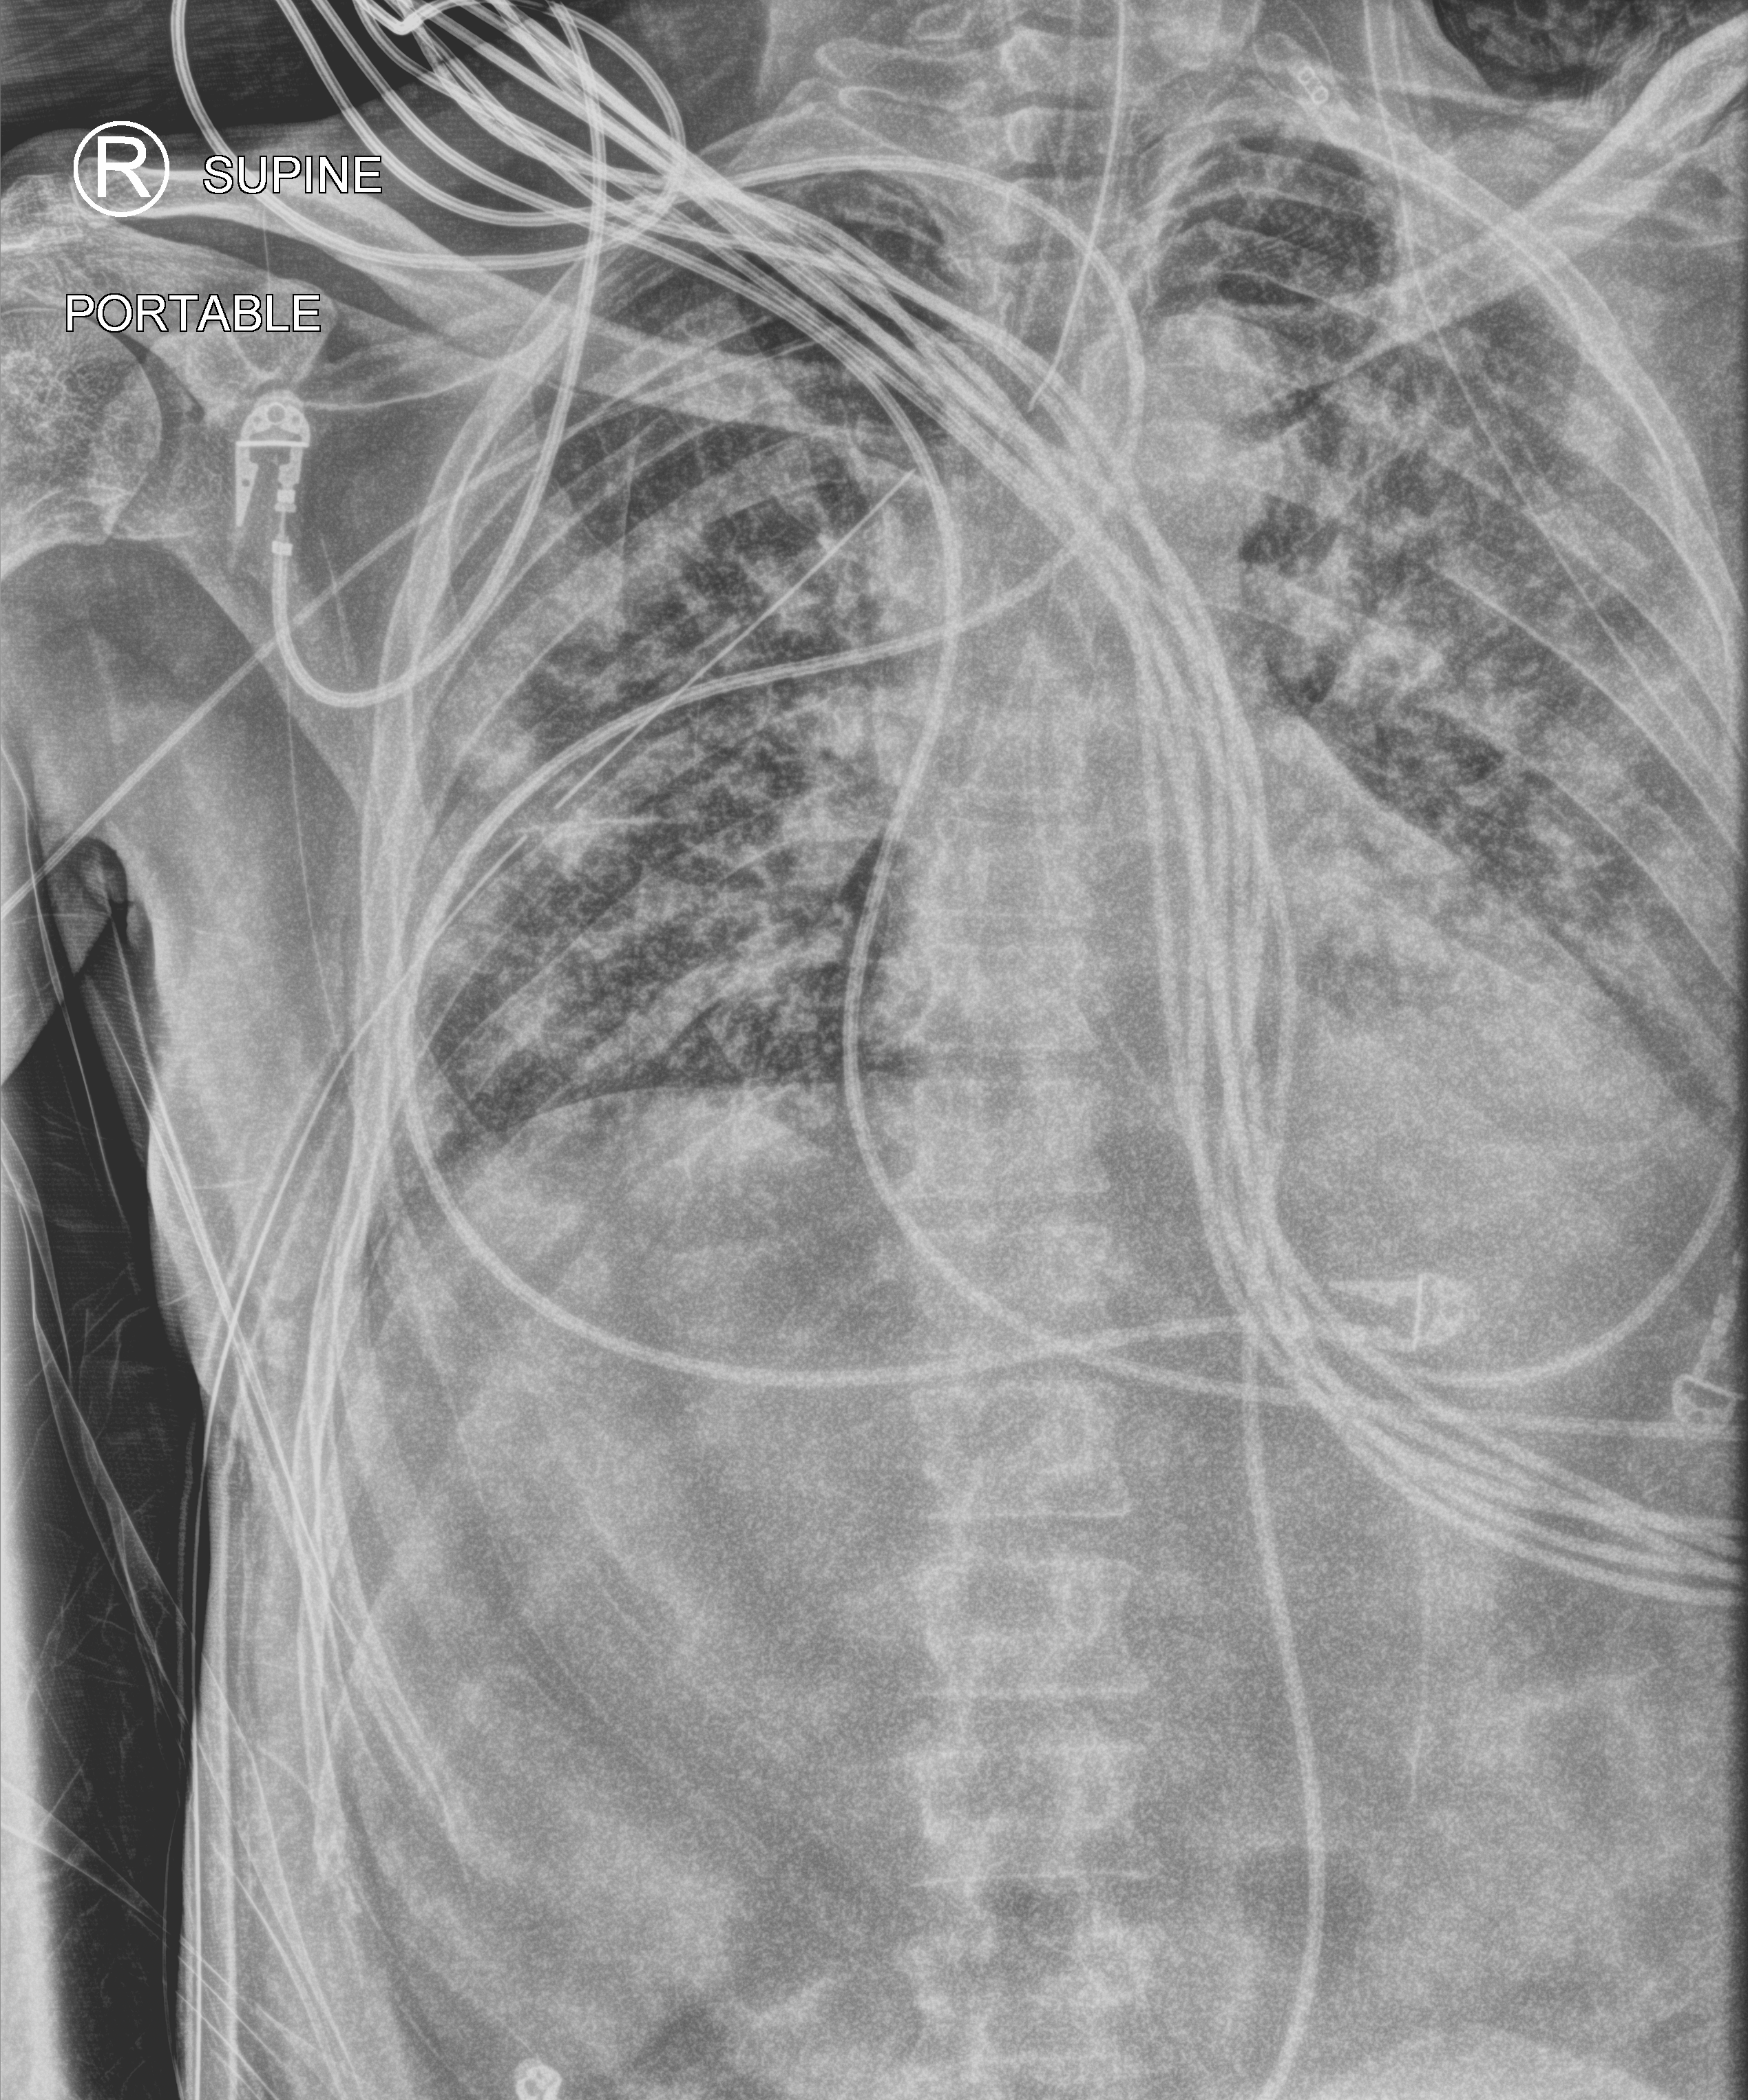
Bedside chest radiograph (computed radiography); anteroposterior (AP) projection. Male patient hospitalised with COVID-19, age 18–59 years.
Admission-level facts for this patient (not findings on this image; timing relative to this image not recorded):
- smoking status (admission record): never
- admitted to intensive care during this hospital stay: yes
- length of hospital stay: 41 days